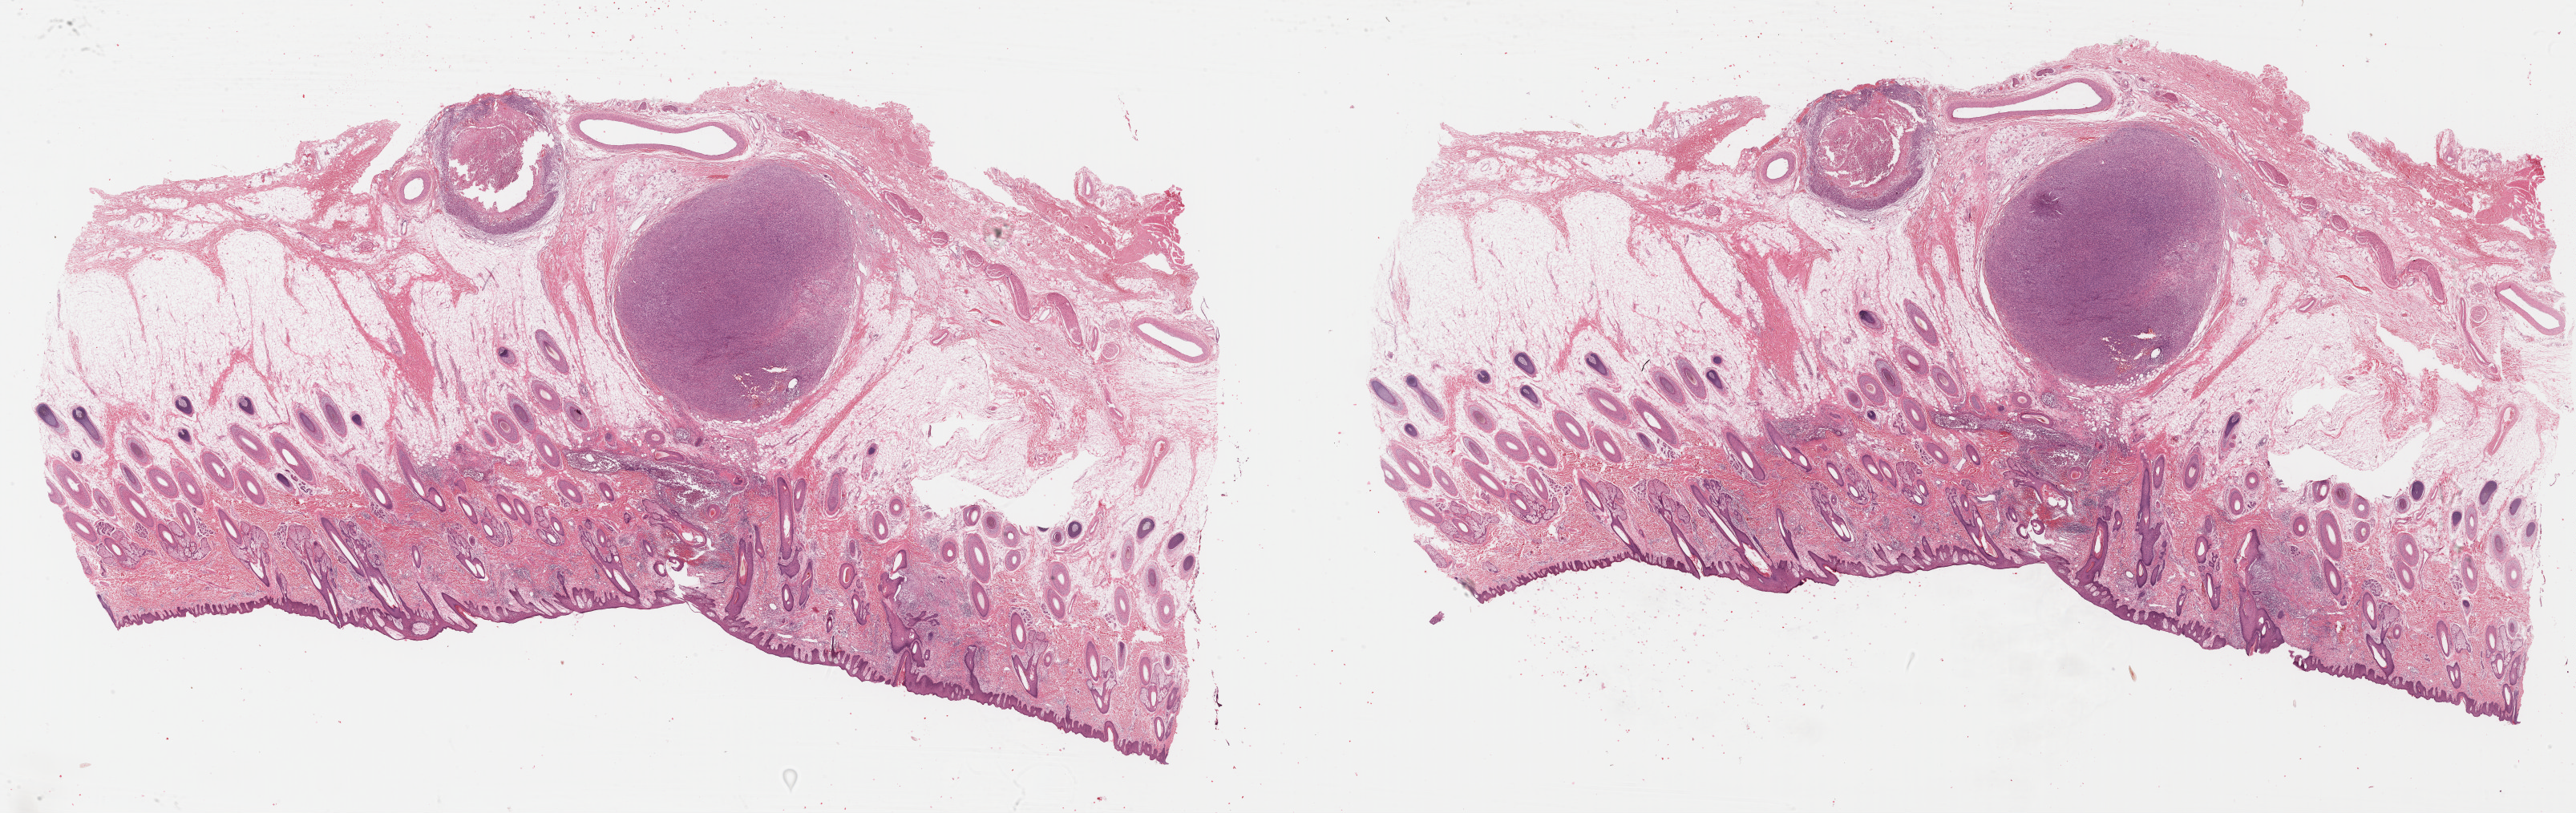
H&E whole-slide image — shown as a low-resolution overview of the whole scanned area (about 50.5 x 15.9 mm), formalin-fixed paraffin-embedded (FFPE) diagnostic section, metastatic tumour sample, sampled site not recorded. Patient: male, age at initial diagnosis 19 years.
* this section: metastatic tumour tissue
* patient diagnosis: Malignant melanoma, NOS